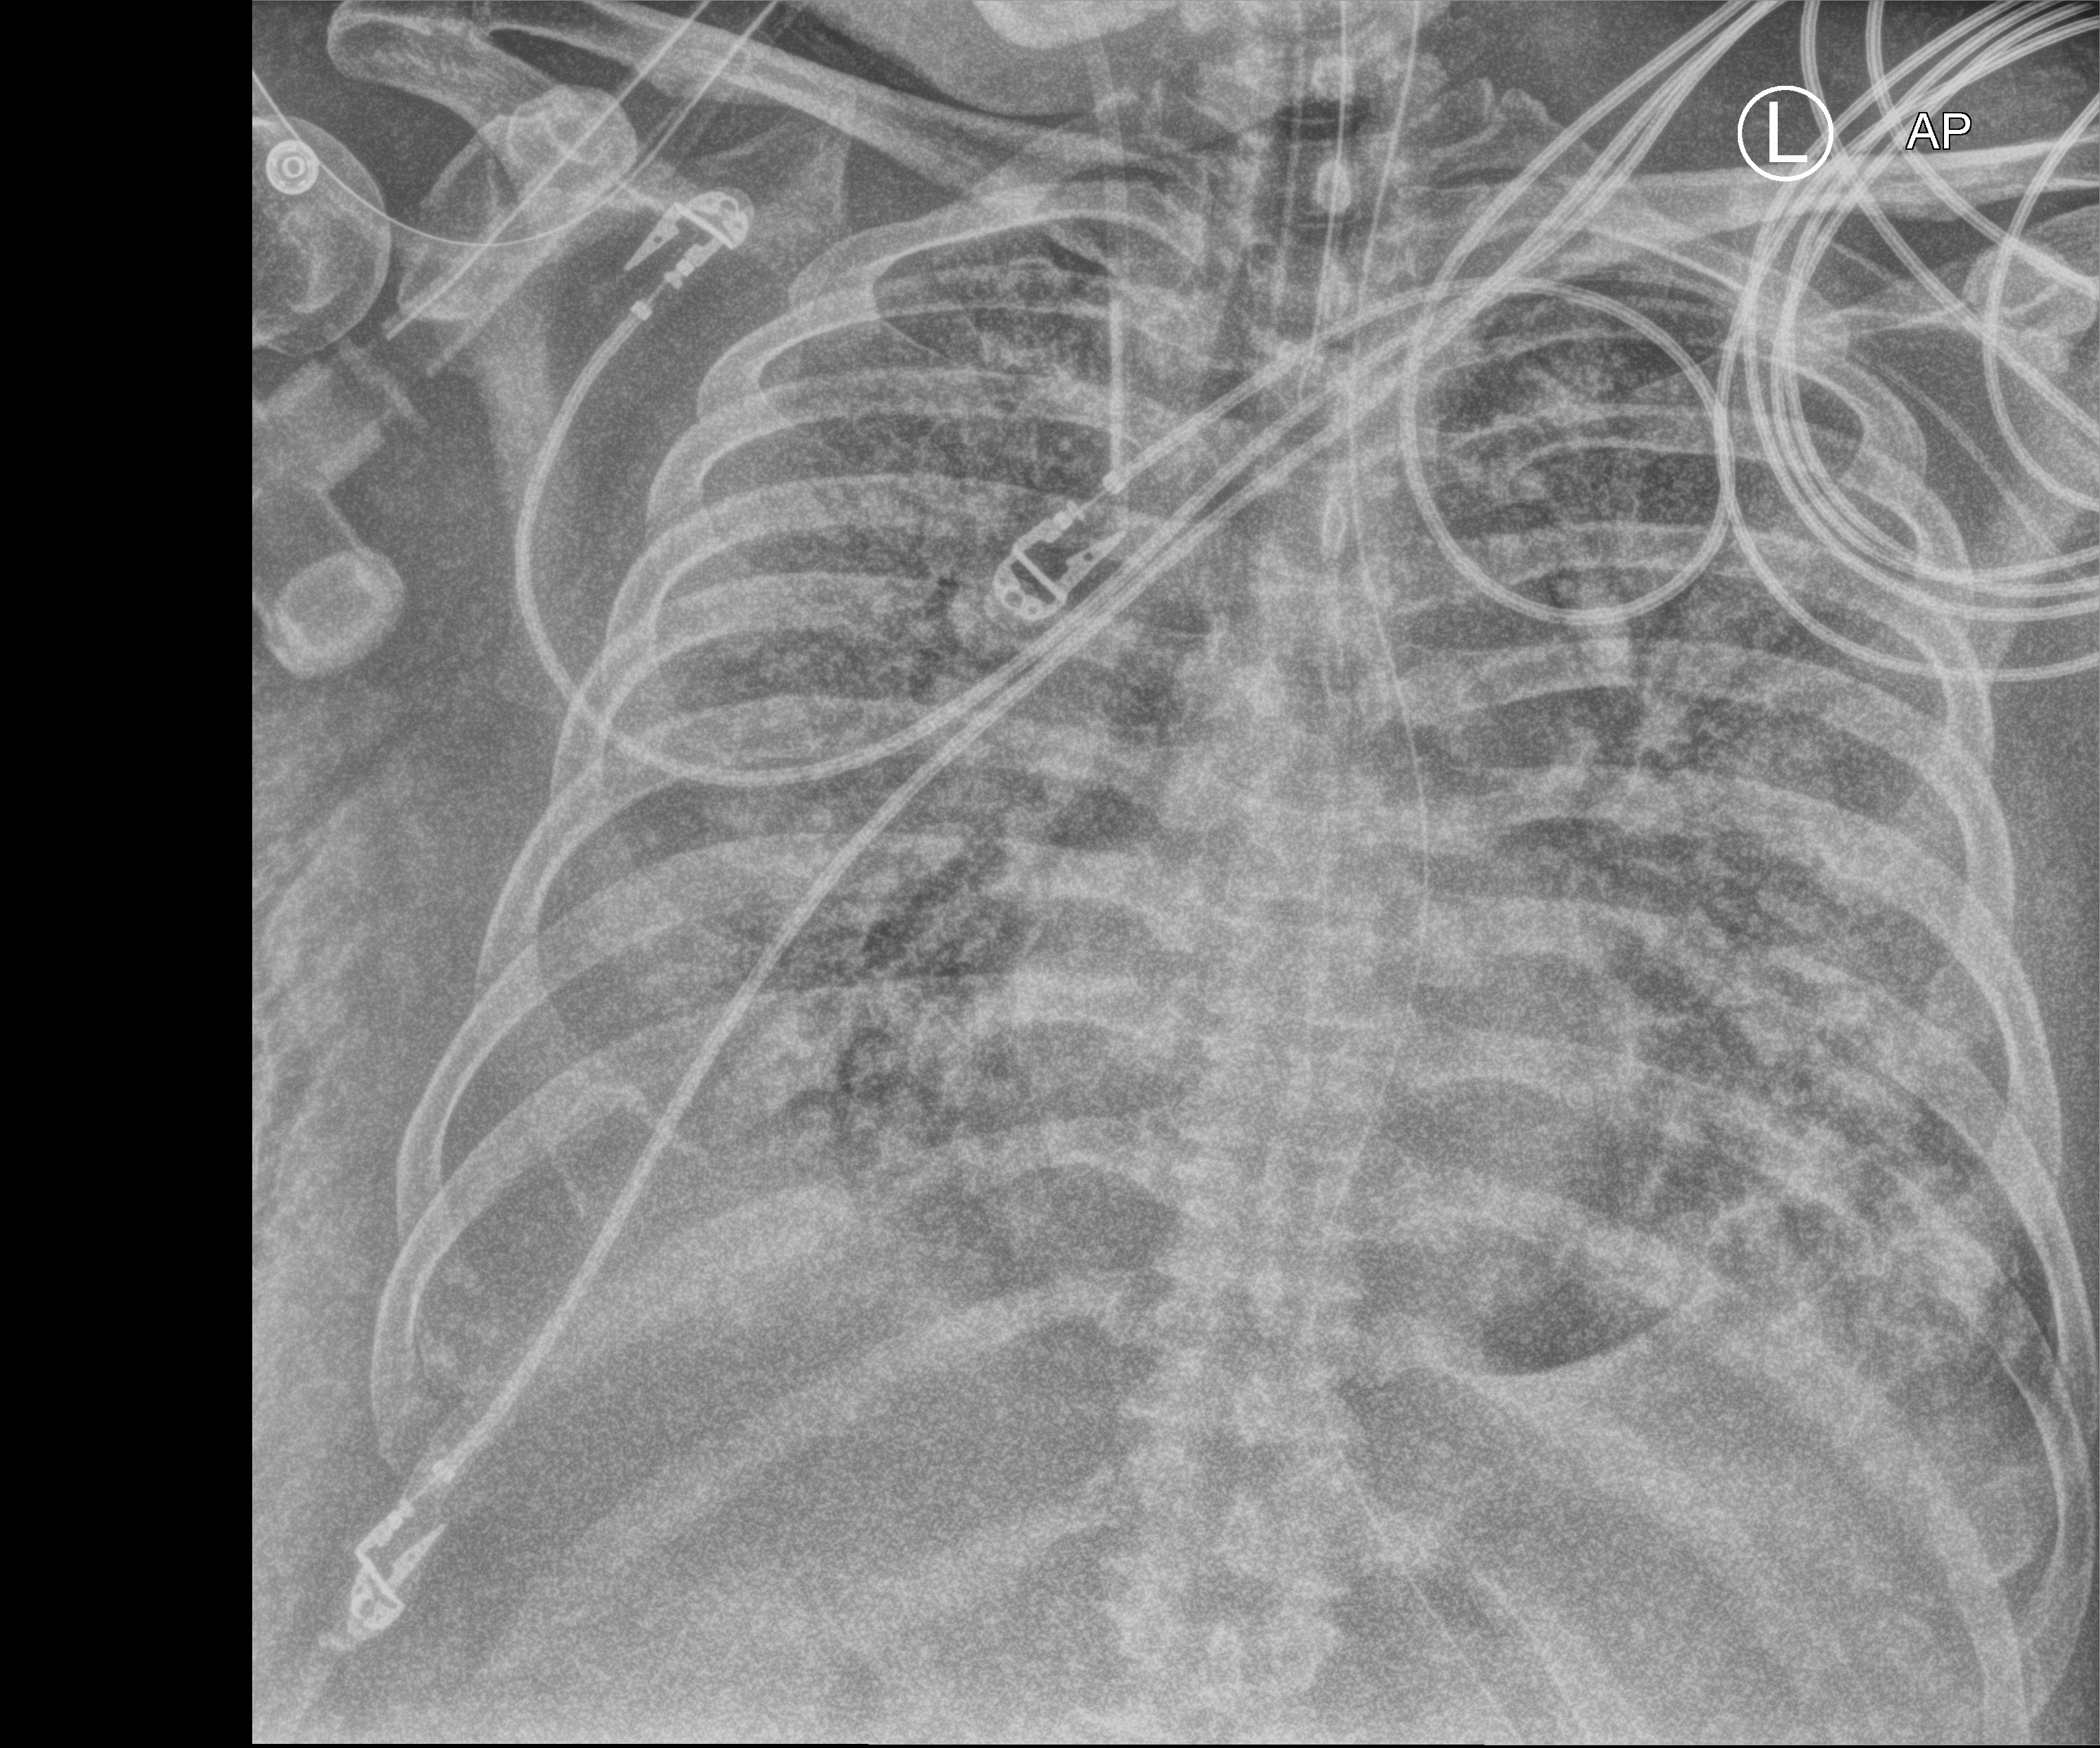
Chest X-ray (portable); anteroposterior (AP) projection. Male patient hospitalised with COVID-19, age 60–74 years.
Hospital-stay facts (about this admission, not read from this image; timing relative to this image not recorded): admitted to intensive care during this hospital stay: yes; COPD (admission record): no; mechanically ventilated during this hospital stay: yes.